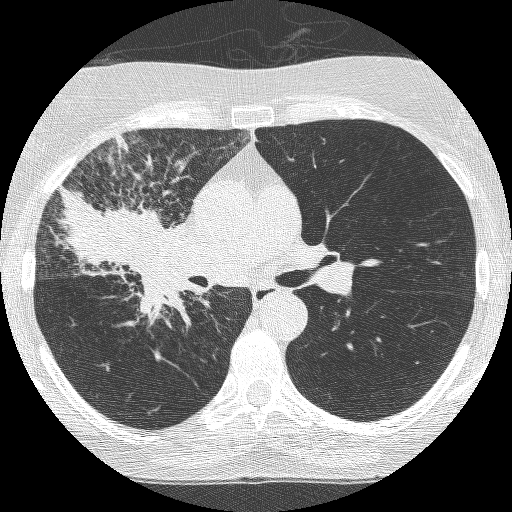
Chest CT (low-dose screening protocol), one axial image, third annual screen, lung window (W 1500 / L -600 HU), 1.25 mm slice thickness, slice 152 of 253 in the series. Female, age 64 years at enrolment. Former smoker at enrolment.
Lesion marked by an expert reader, bounding box <71,189,202,321> (left, top, right, bottom; pixels). Reader record for this screening exam (exam-level; its link to the box is not recorded): non-calcified nodule or mass ≥4 mm, right upper lobe, 49 × 43 mm, spiculated (stellate) margins, soft tissue attenuation, pre-existing on the prior screen: yes; interval growth: yes. Participant outcome: lung cancer diagnosed 7 days after this screen — adenocarcinoma, NOS, right upper lobe, right middle lobe, right hilum, stage IV (AJCC 6th edition), 85 mm at pathology.